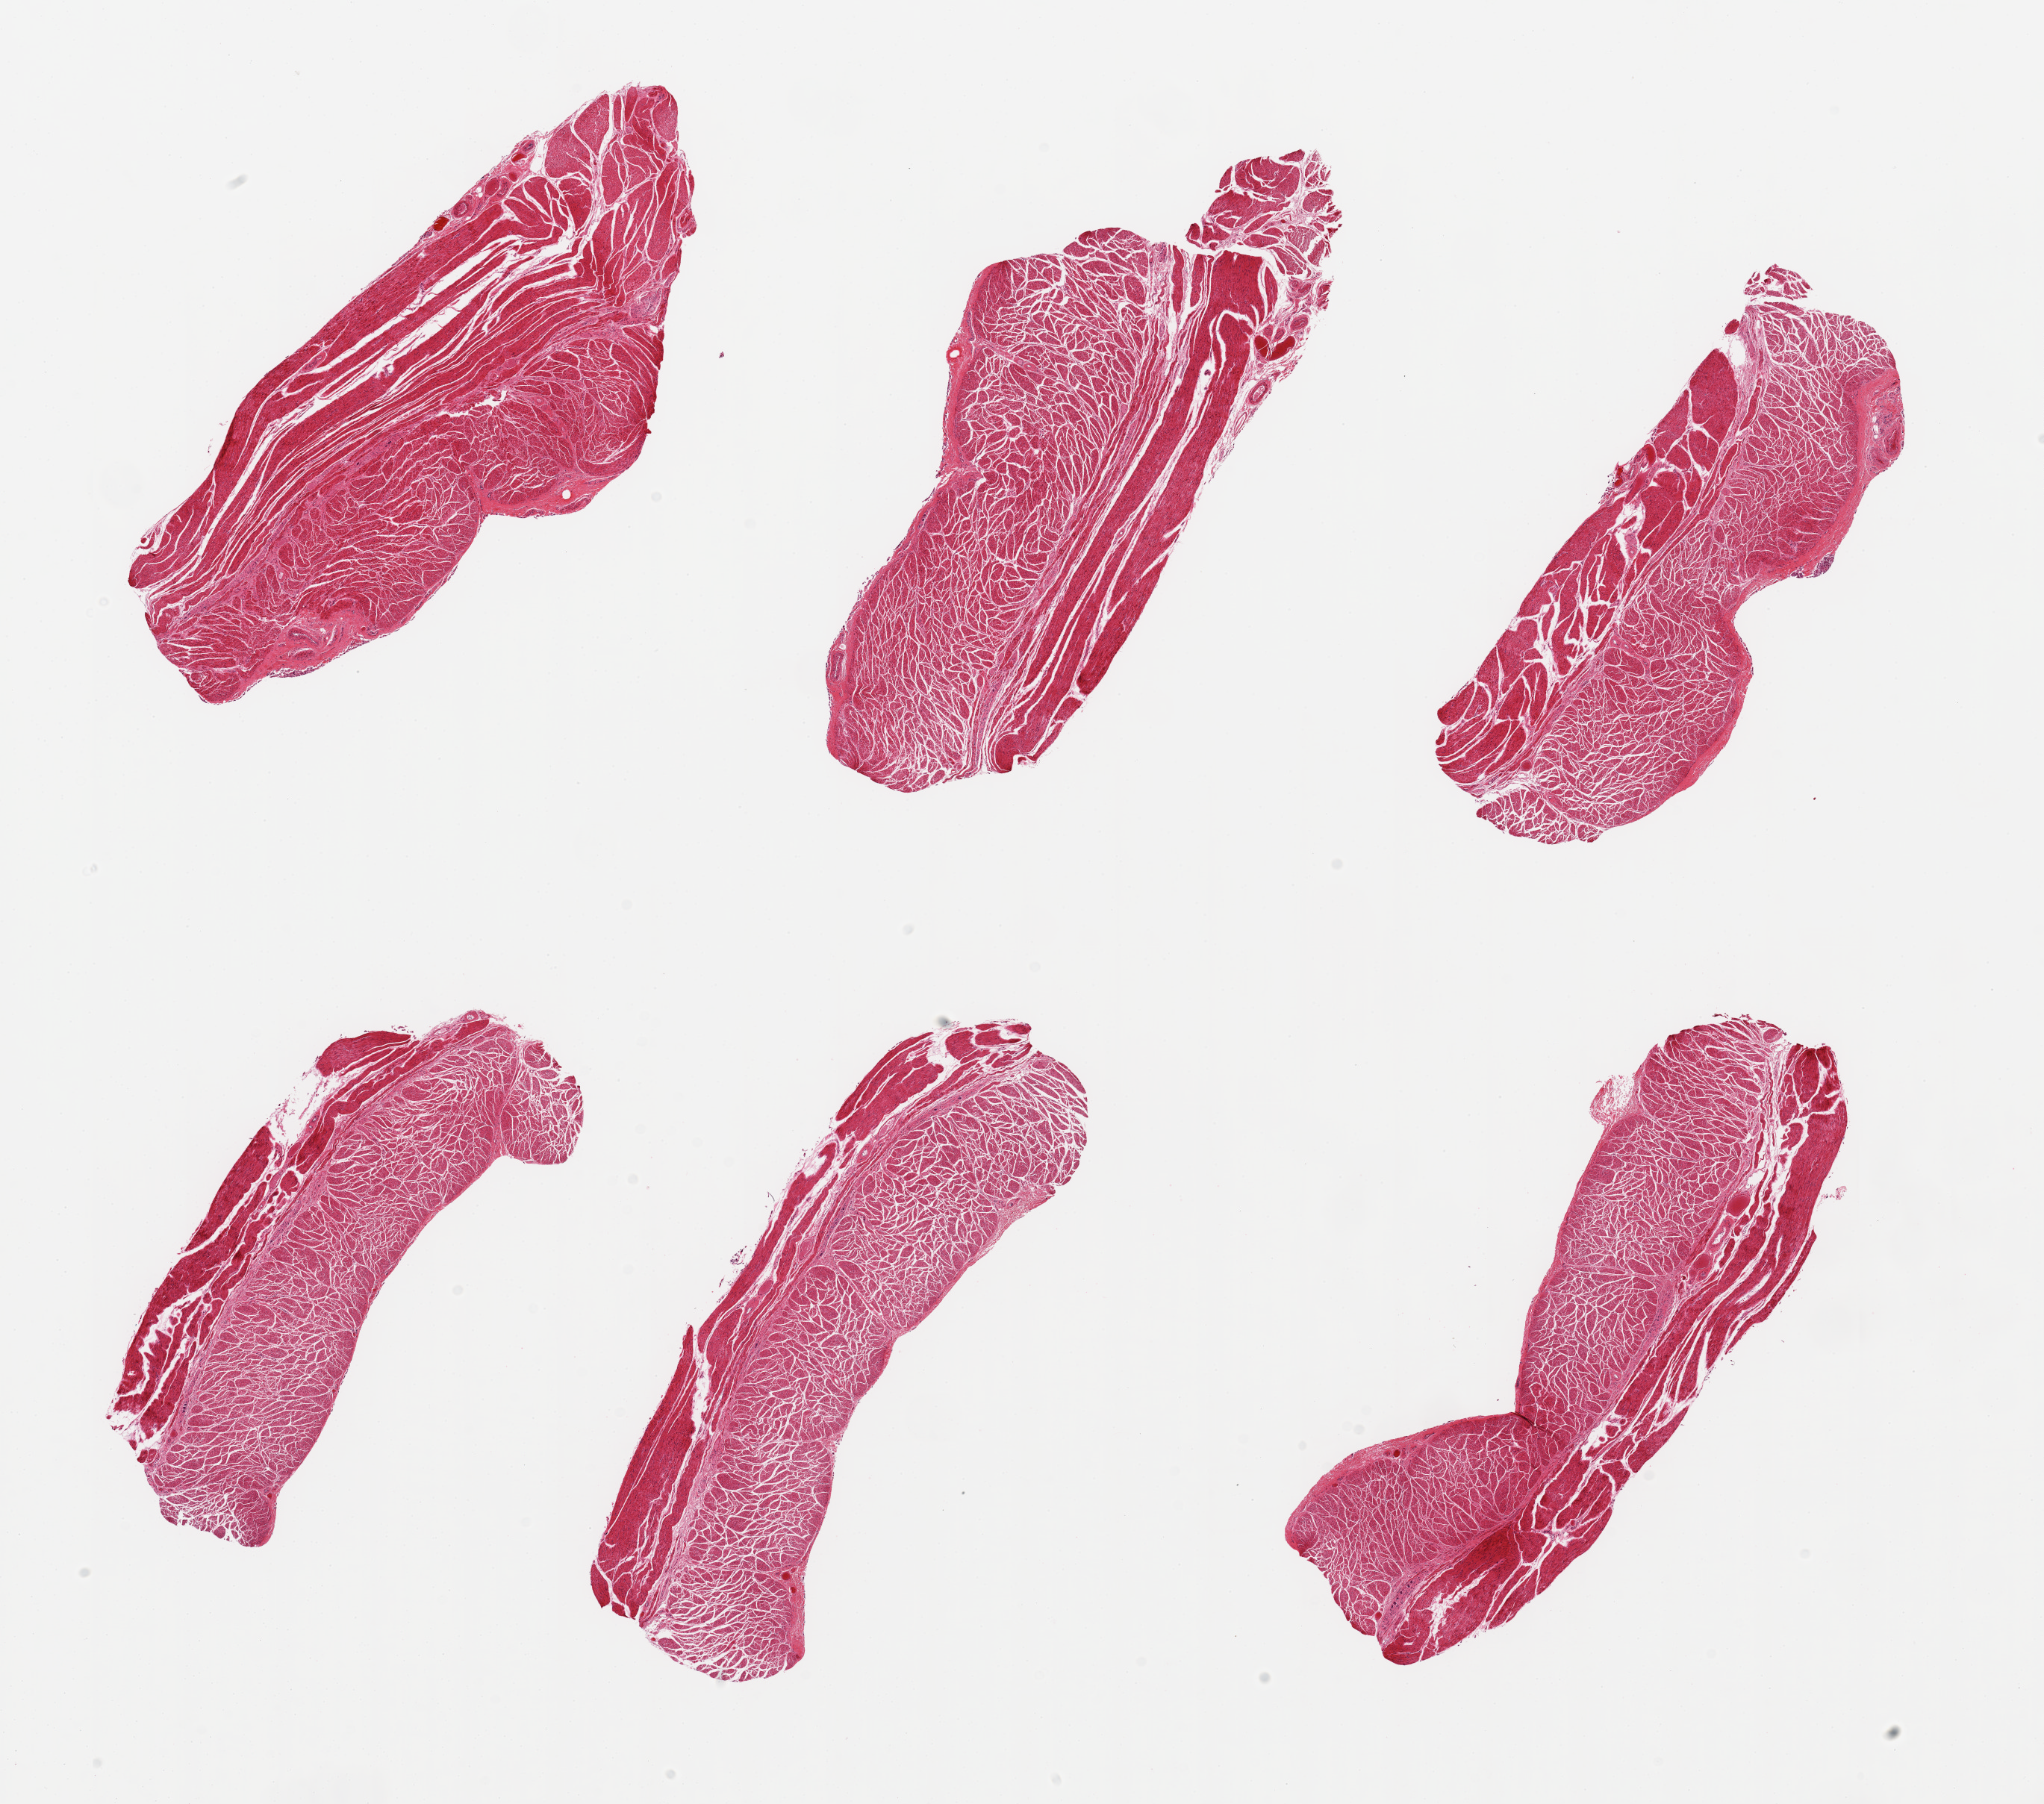
Digitized haematoxylin and eosin-stained section, brightfield, a low-resolution overview of the entire scanned area, about 21.7 x 19.1 mm, PAXgene-fixed, paraffin-embedded tissue, target tissue: esophageal muscle, donor tissue sample. Donor: male.
Reviewer comment on this tissue sample: 6 pieces; well trimmed.